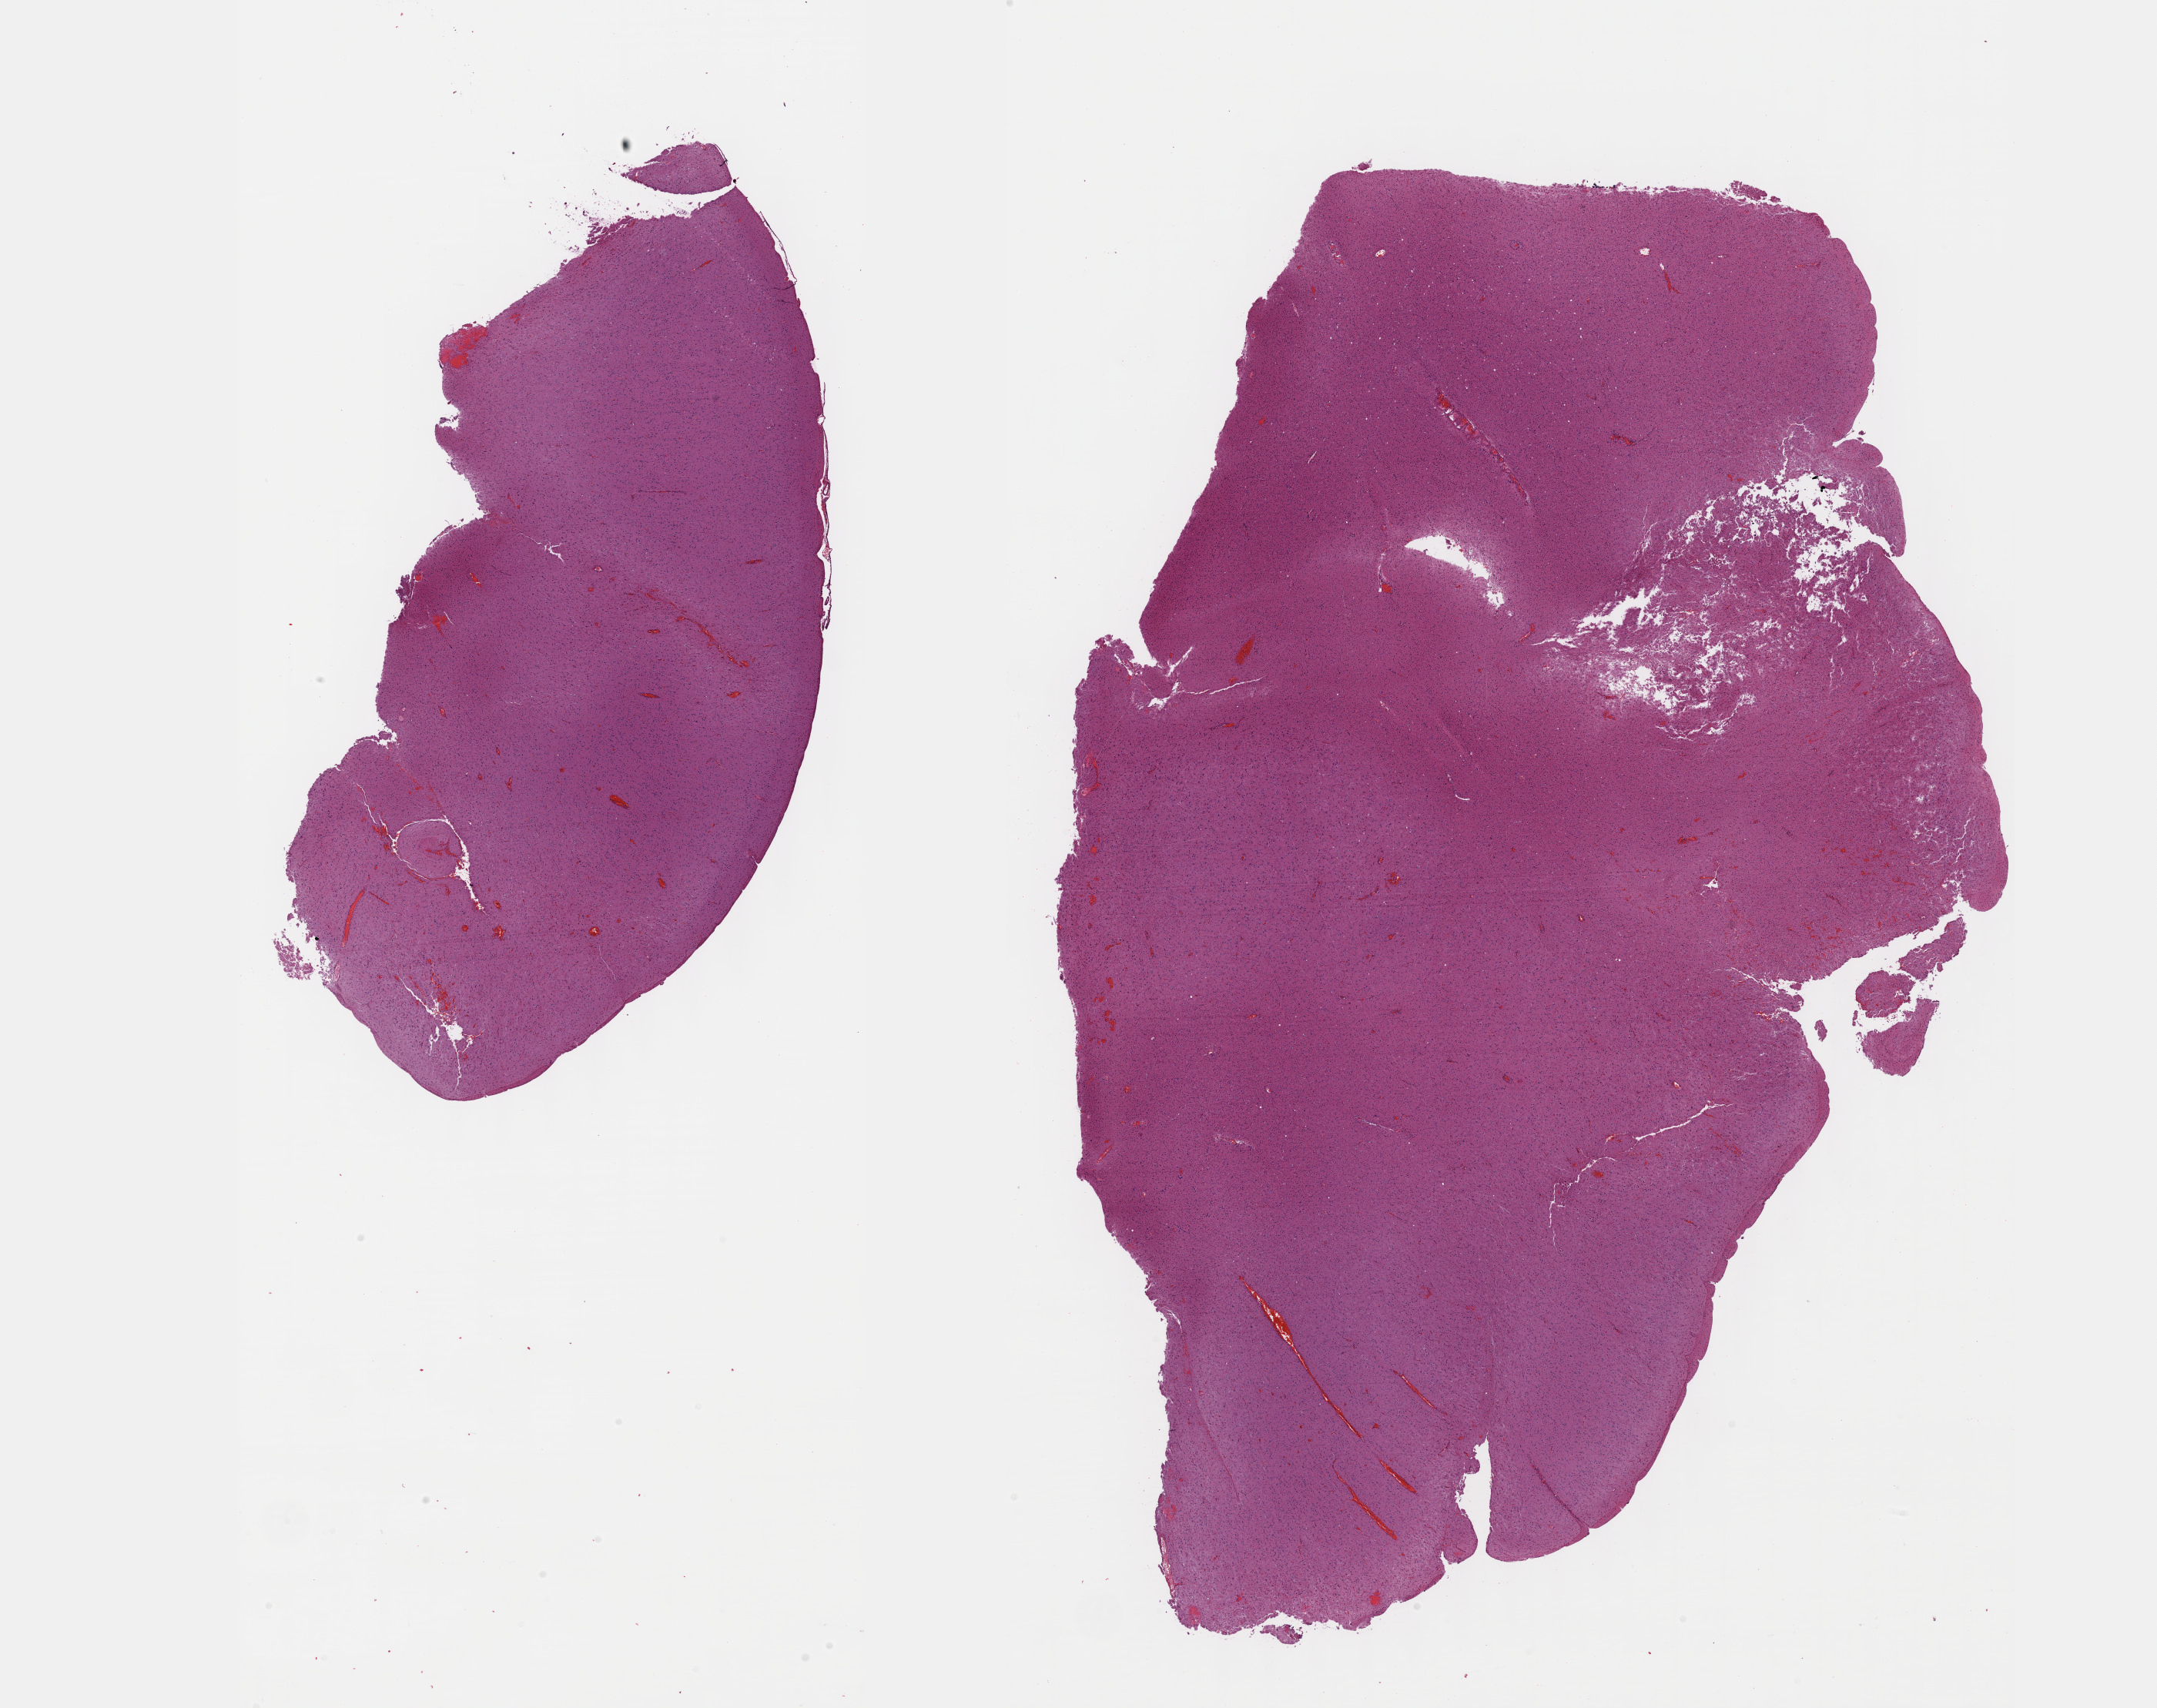
H&E-stained whole-slide image — shown as a low-resolution overview of the whole scanned area (about 22.6 x 17.9 mm), FFPE section, primary tumour sample from the brain. Male patient; age at initial diagnosis 62 years. Histologic grade: G2 (moderately differentiated).
Pathologic diagnosis: Astrocytoma, NOS. Laterality: left.